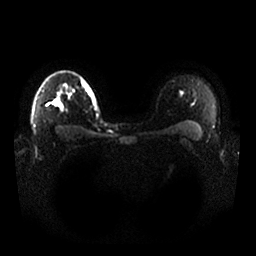
Breast MRI, one axial slice. Position 22 of 25 along the scan axis. Diffusion-weighted series; image 2 of 4 stored at this slice position (different b-values; order by instance number). 1.5 T. 256 × 256 image matrix, field of view 370 × 370 mm. Female patient.
Outlined on this slice (expert manual segmentation):
- tumour on diffusion-weighted imaging: box from (x=54, y=101) to (x=62, y=107) px